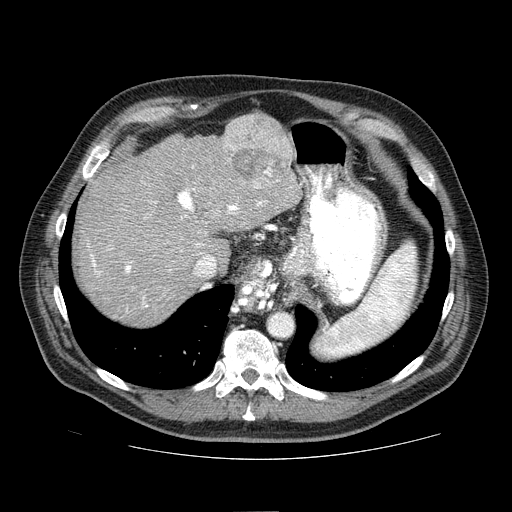
Contrast-enhanced abdominal CT (liver protocol), one axial slice; slice 57 of 81 in the series (ordered by position); reconstruction kernel STANDARD; 100 kVp; one of 2 acquisitions stored at this slice position; soft-tissue window (W 400 / L 40 HU); 2.5 mm slice thickness; 512 × 512 image matrix. Case-level facts recorded for this patient, not image findings: diagnosis: hepatocellular carcinoma (patient treated with transarterial chemoembolisation; whether this scan precedes or follows treatment is not stated here); TNM stage (as recorded): Stage-IIIA; Child-Pugh class: A; tumour differentiation: well differentiated; tumour nodularity: multinodular.
Annotated regions visible in this slice (semi-automatic segmentation, software-assisted and operator-edited):
- abdominal aorta: box from (x=270, y=314) to (x=293, y=337) px
- liver parenchyma outside the tumour (the mass and vessels are separate outlines, so this box may not span the whole liver): (x=74, y=114)–(x=300, y=324)
- mass: (x=219, y=114)–(x=292, y=187)
- liver vessels: (x=88, y=166)–(x=263, y=311)